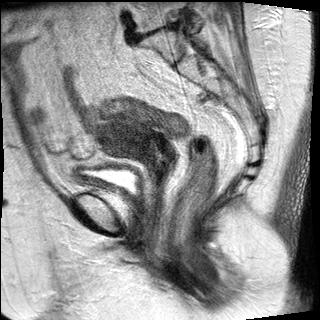
Pelvic MRI for cervical cancer, one sagittal slice. Slice 13 of 27 in the series (ordered by position). T2-weighted. 1.5 T. TE 89 ms, TR 2740 ms. 4 mm slice thickness. 320 × 320 image matrix, field of view 260 × 260 mm. Female patient, age 67 years.
Structures marked on this image (expert manual segmentation):
- uterus and cervix: box from (x=96, y=118) to (x=177, y=179) px